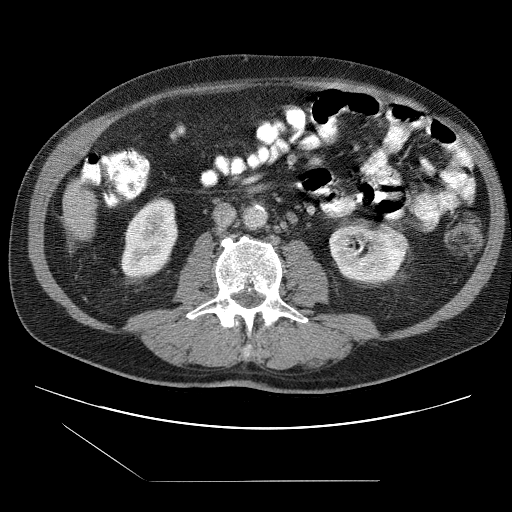
Contrast-enhanced abdominal CT (liver protocol), one axial slice. Position 10 of 109 along the scan axis. Reconstruction kernel STANDARD. 120 kVp. One of 2 acquisitions stored at this slice position. Soft-tissue window (W 400 / L 40 HU). 2.5 mm slice thickness. 512 × 512 image matrix, field of view 400 × 400 mm. From the clinical record (not read from this slice): diagnosis: hepatocellular carcinoma (patient treated with transarterial chemoembolisation; whether this scan precedes or follows treatment is not stated here); TNM stage (as recorded): Stage-IIIB; Child-Pugh class: A; tumour differentiation: well differentiated.
Structures marked on this image (semi-automatic segmentation, software-assisted and operator-edited):
- liver parenchyma outside the tumour (the mass and vessels are separate outlines, so this box may not span the whole liver): box from (x=62, y=175) to (x=100, y=240) px
- liver vessels: (x=82, y=176)–(x=99, y=182)